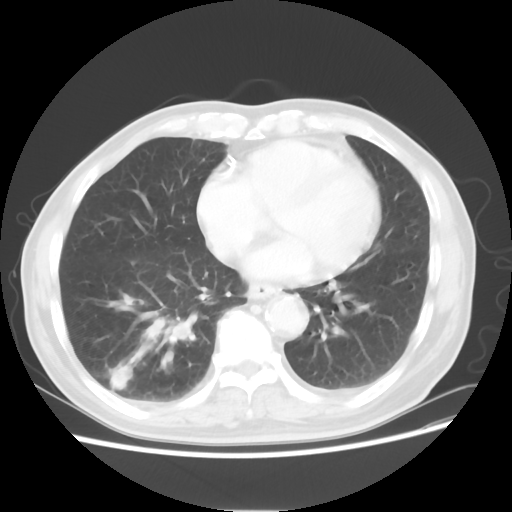
Chest CT, one axial slice. Position 21 of 58 along the scan axis. 120 kVp. Lung window (W 1500 / L -600 HU). 512 × 512 image matrix. Male patient, age 74 years. Case-level facts recorded for this patient, not image findings: clinical TNM (as recorded): T1c N1 M1.
Outlined on this slice (rectangle marked by the reading radiologist):
- lung tumour (recorded histology: adenocarcinoma): bounding box <126,292,205,367> (left, top, right, bottom; pixels)